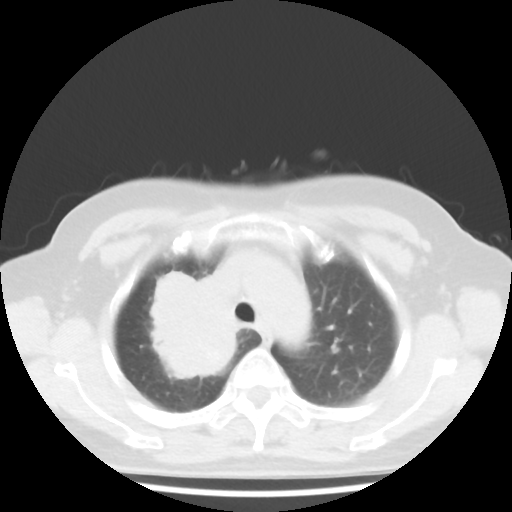
Chest CT, one axial slice. Reconstruction kernel STANDARD. Lung window (W 1500 / L -600 HU). 5 mm slice thickness. 512 × 512 image matrix. Patient: female, 62 years. Case-level facts recorded for this patient, not image findings: clinical TNM (as recorded): T3 N0 M0; histopathological grade: G3.
Outlined on this slice (bounding box drawn by a radiologist):
- lung tumour (recorded histology: small cell carcinoma): bounding box <137,265,237,386> (left, top, right, bottom; pixels)